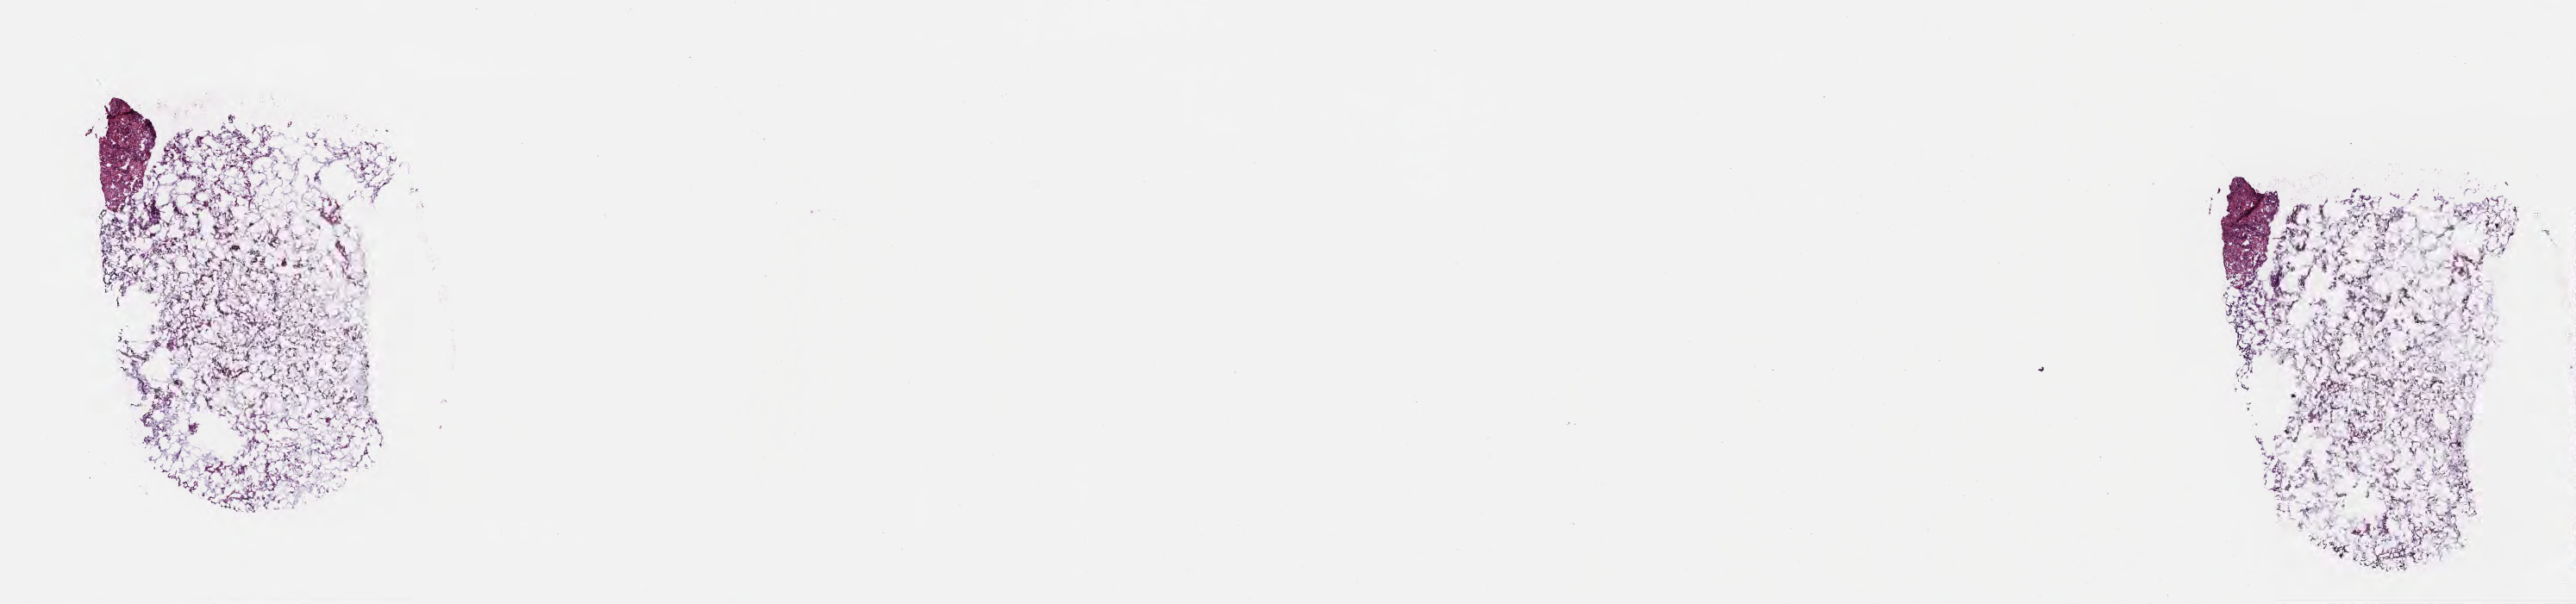
Haematoxylin and eosin whole-slide image, low-resolution overview of the scanned area, about 24.1 x 5.7 mm; frozen section (tissue freezing medium); specimen: primary tumor; anatomic site: sigmoid colon. Patient sex: female. Tumor grade: G4 (undifferentiated). Pathologist review of this section (percent, as recorded): tumor cells 80%, tumor nuclei 80%, stromal cells 20%, necrosis 0%, normal cells 0%. Infiltration values recorded for this section: lymphocyte infiltration 3%, monocyte infiltration 6%, neutrophil infiltration 6%.
Section: bottom of the tissue portion. Histologic diagnosis: Adenocarcinoma, NOS.